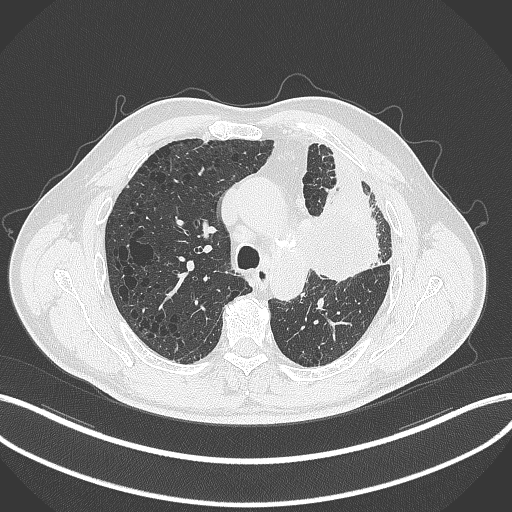
Chest CT, one axial slice. Position 216 of 297 along the scan axis. Reconstruction kernel B70f. 120 kVp. Lung window (W 1500 / L -600 HU). 512 × 512 image matrix. Male patient, age 68 years. Case-level facts recorded for this patient, not image findings: clinical TNM (as recorded): T3 N3 M1.
Structures marked on this image (bounding box drawn by a radiologist):
- lung tumour (recorded histology: adenocarcinoma): bounding box <317,168,381,280> (left, top, right, bottom; pixels)